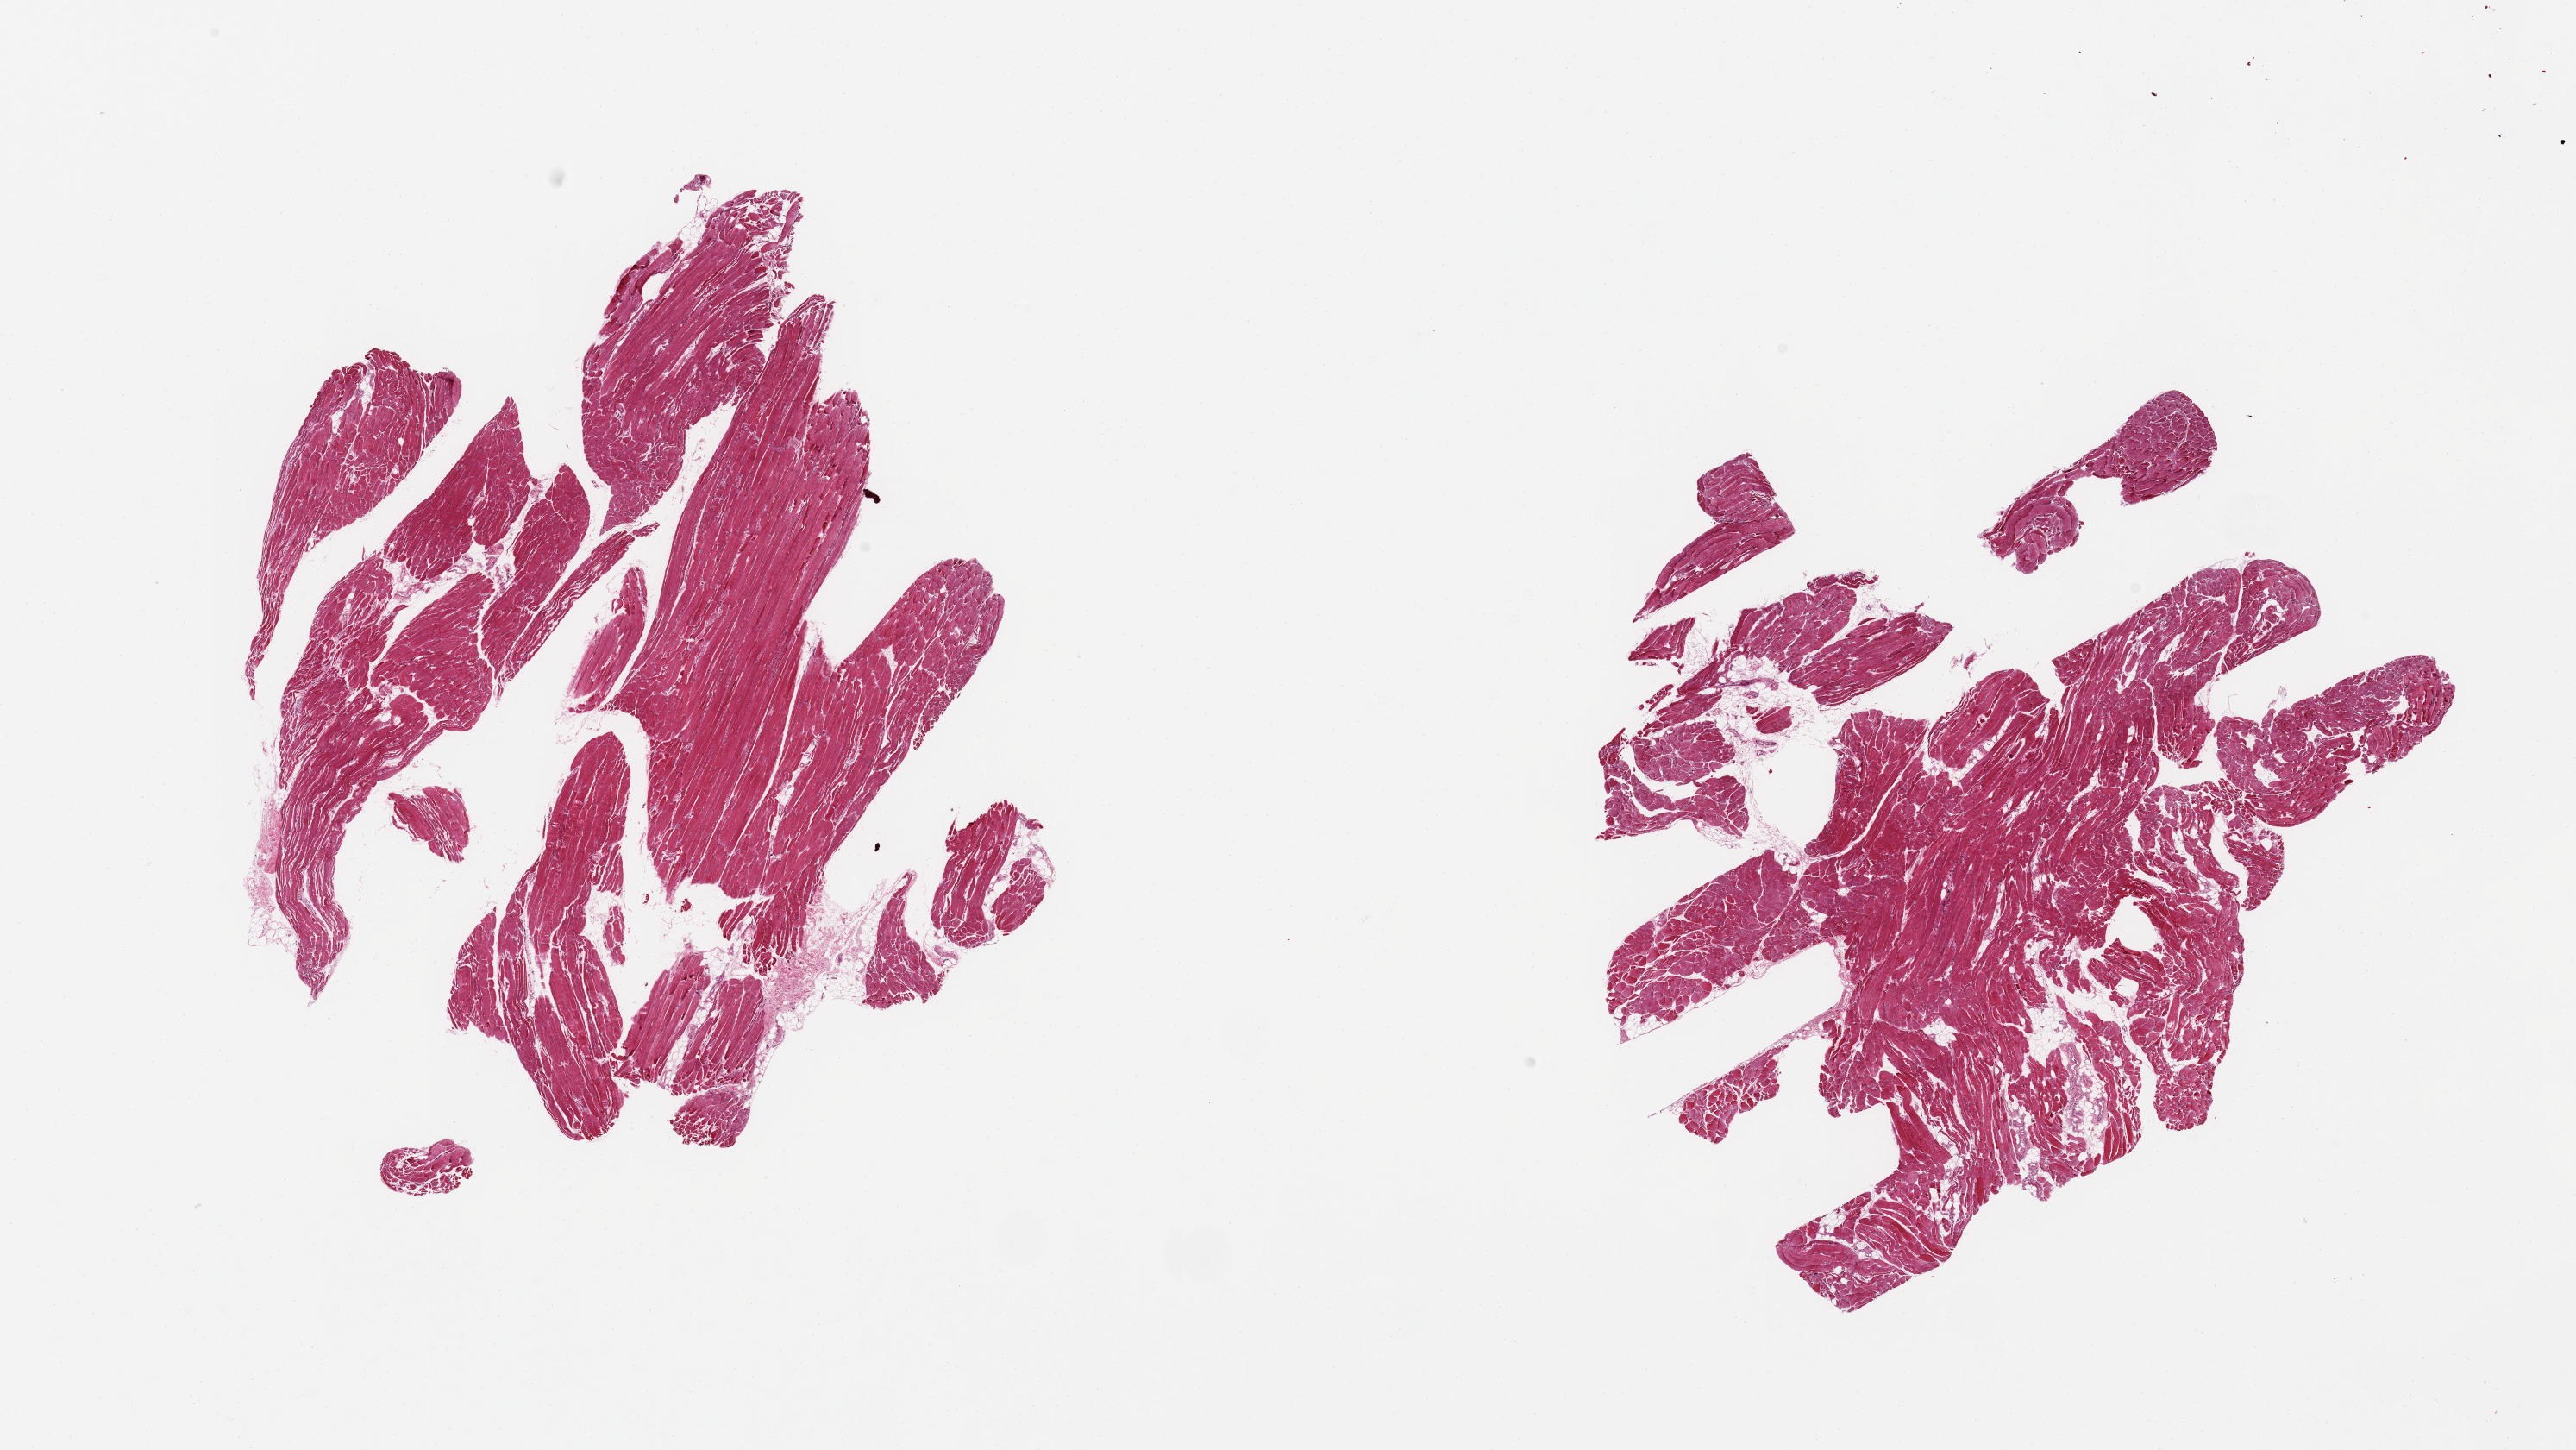
Haematoxylin and eosin whole-slide image, low-resolution overview of the scanned area, about 23.6 x 13.3 mm (from a 20x scan). PAXgene-fixed, paraffin-embedded tissue. Section of skeletal muscle (target tissue). Tissue donor sample. Donor: male.
Review note (as recorded): 2 fragmented pieces; patchy atrophy.